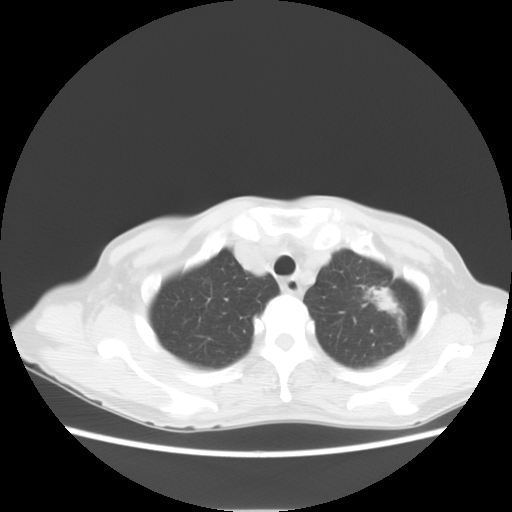
Chest CT, one axial slice. Position 12 of 14 along the scan axis. Lung window (W 1500 / L -600 HU). 5 mm slice thickness. 512 × 512 image matrix, field of view 350 × 350 mm. Female patient, age 71 years. Case-level facts recorded for this patient, not image findings: clinical TNM (as recorded): T2 N0 M0.
Outlined on this slice (rectangle marked by the reading radiologist):
- lung tumour (recorded histology: adenocarcinoma): bounding box <372,284,401,321> (left, top, right, bottom; pixels)